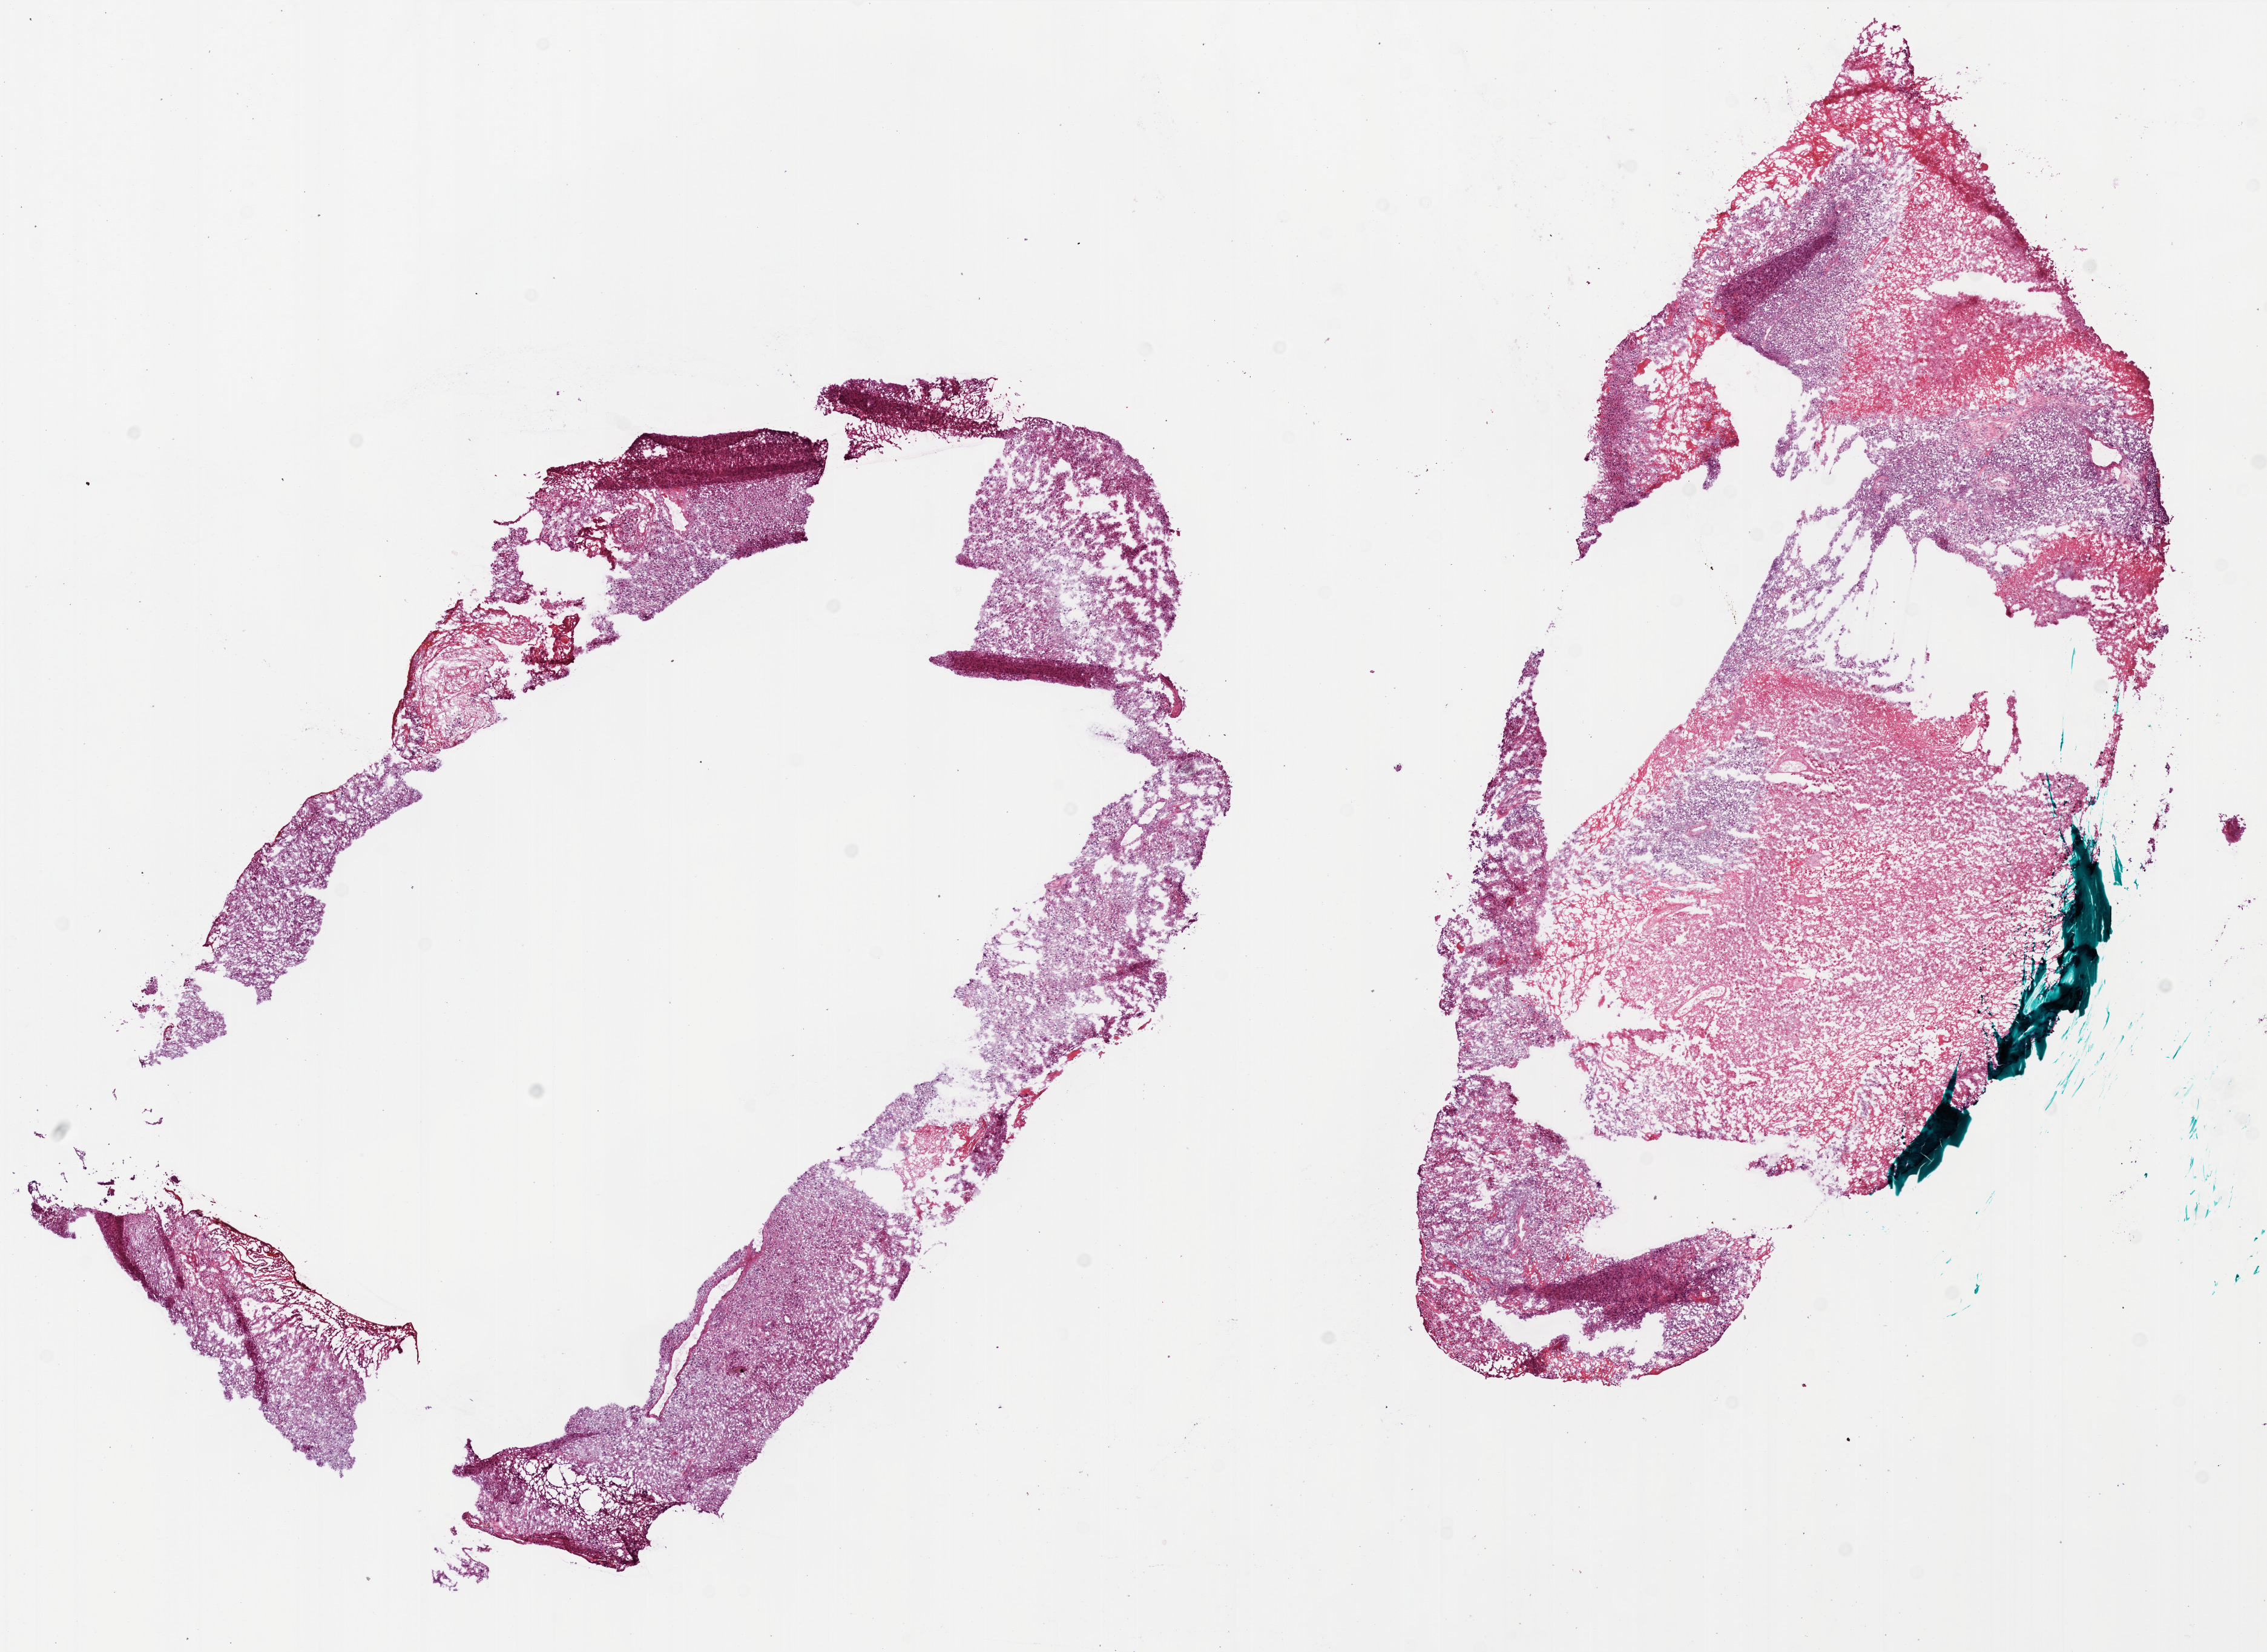
Digitized H&E-stained tissue section (whole slide) — whole scanned area (about 15.0 x 10.9 mm) shown as a low-resolution overview, frozen section, brain, primary tumour sample. Male patient; age at initial diagnosis 78 years. Pathologist review of this section (percent, as recorded): tumour cells 55%, tumour nuclei 90%, normal cells 0%, stromal cells 5%, necrosis 40%.
- diagnosis: Glioblastoma